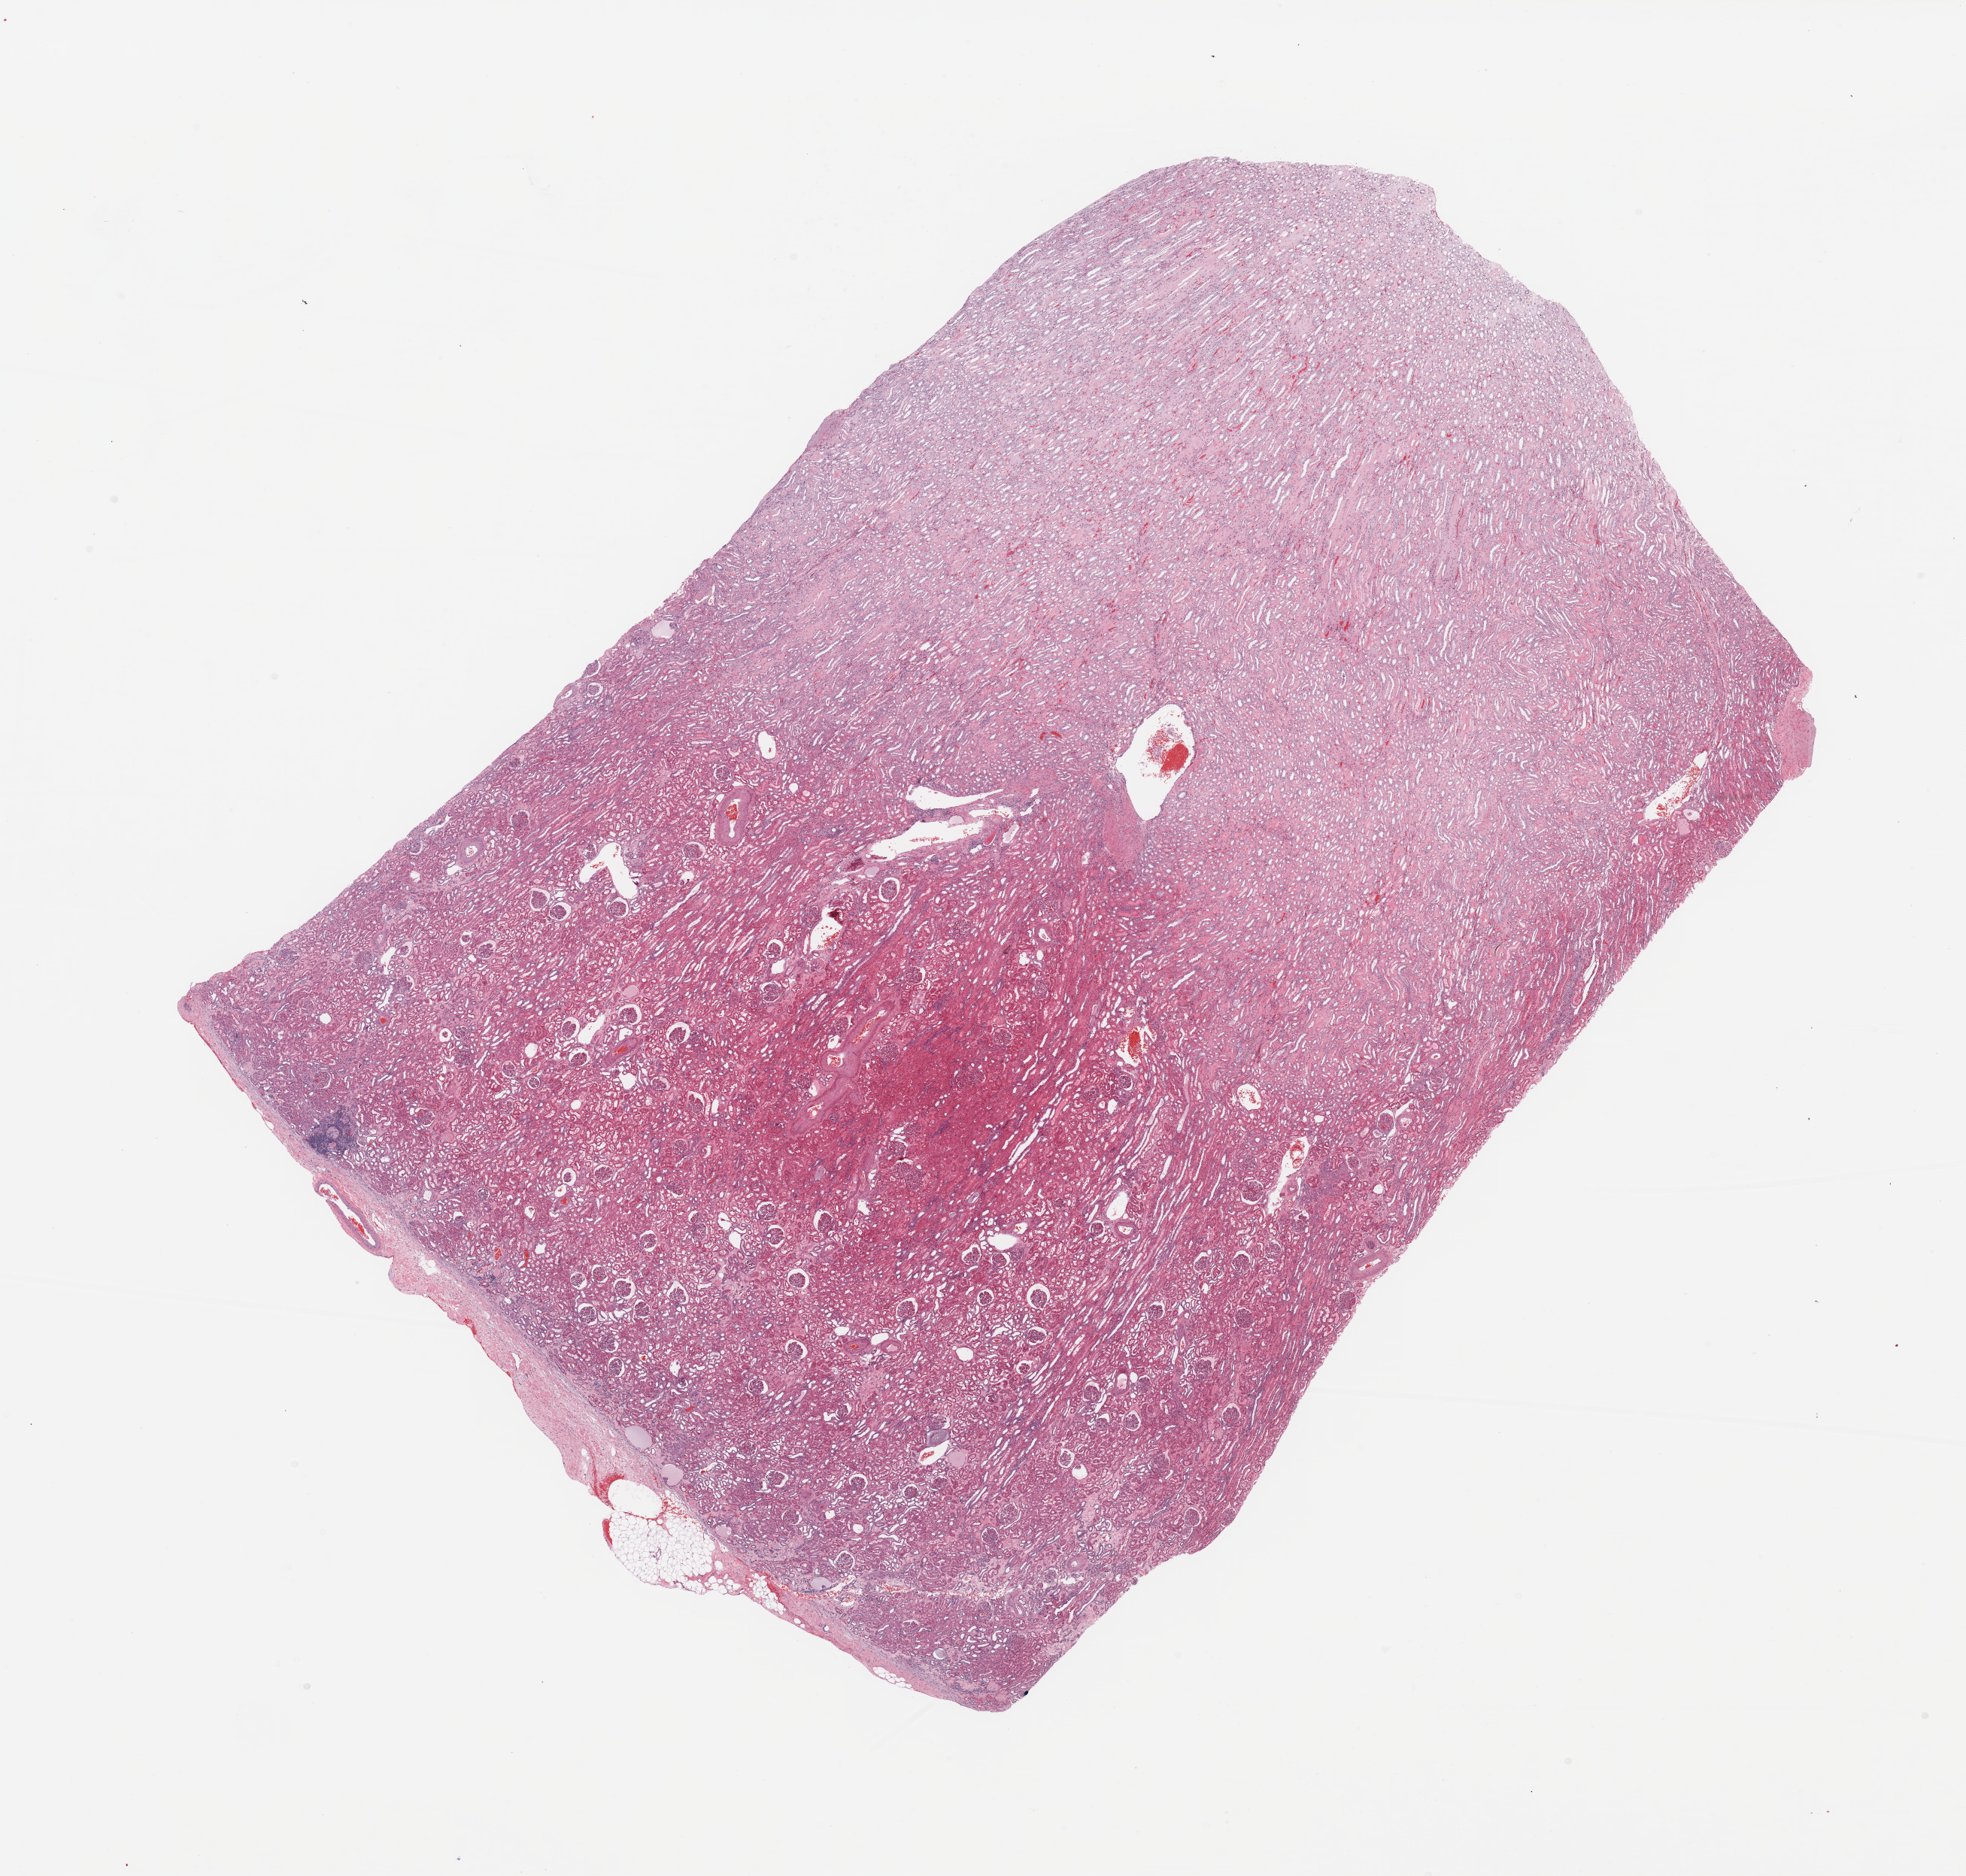
Whole-slide histology image, Hematoxylin and eosin (H&E) stained — whole scanned area (about 20.7 x 19.7 mm) shown as a low-resolution overview. Normal (non-tumour) tissue sample, kidney. 76-year-old male patient.
This section: normal (non-tumour) tissue from the same patient. Patient diagnosis: Renal cell carcinoma, NOS.